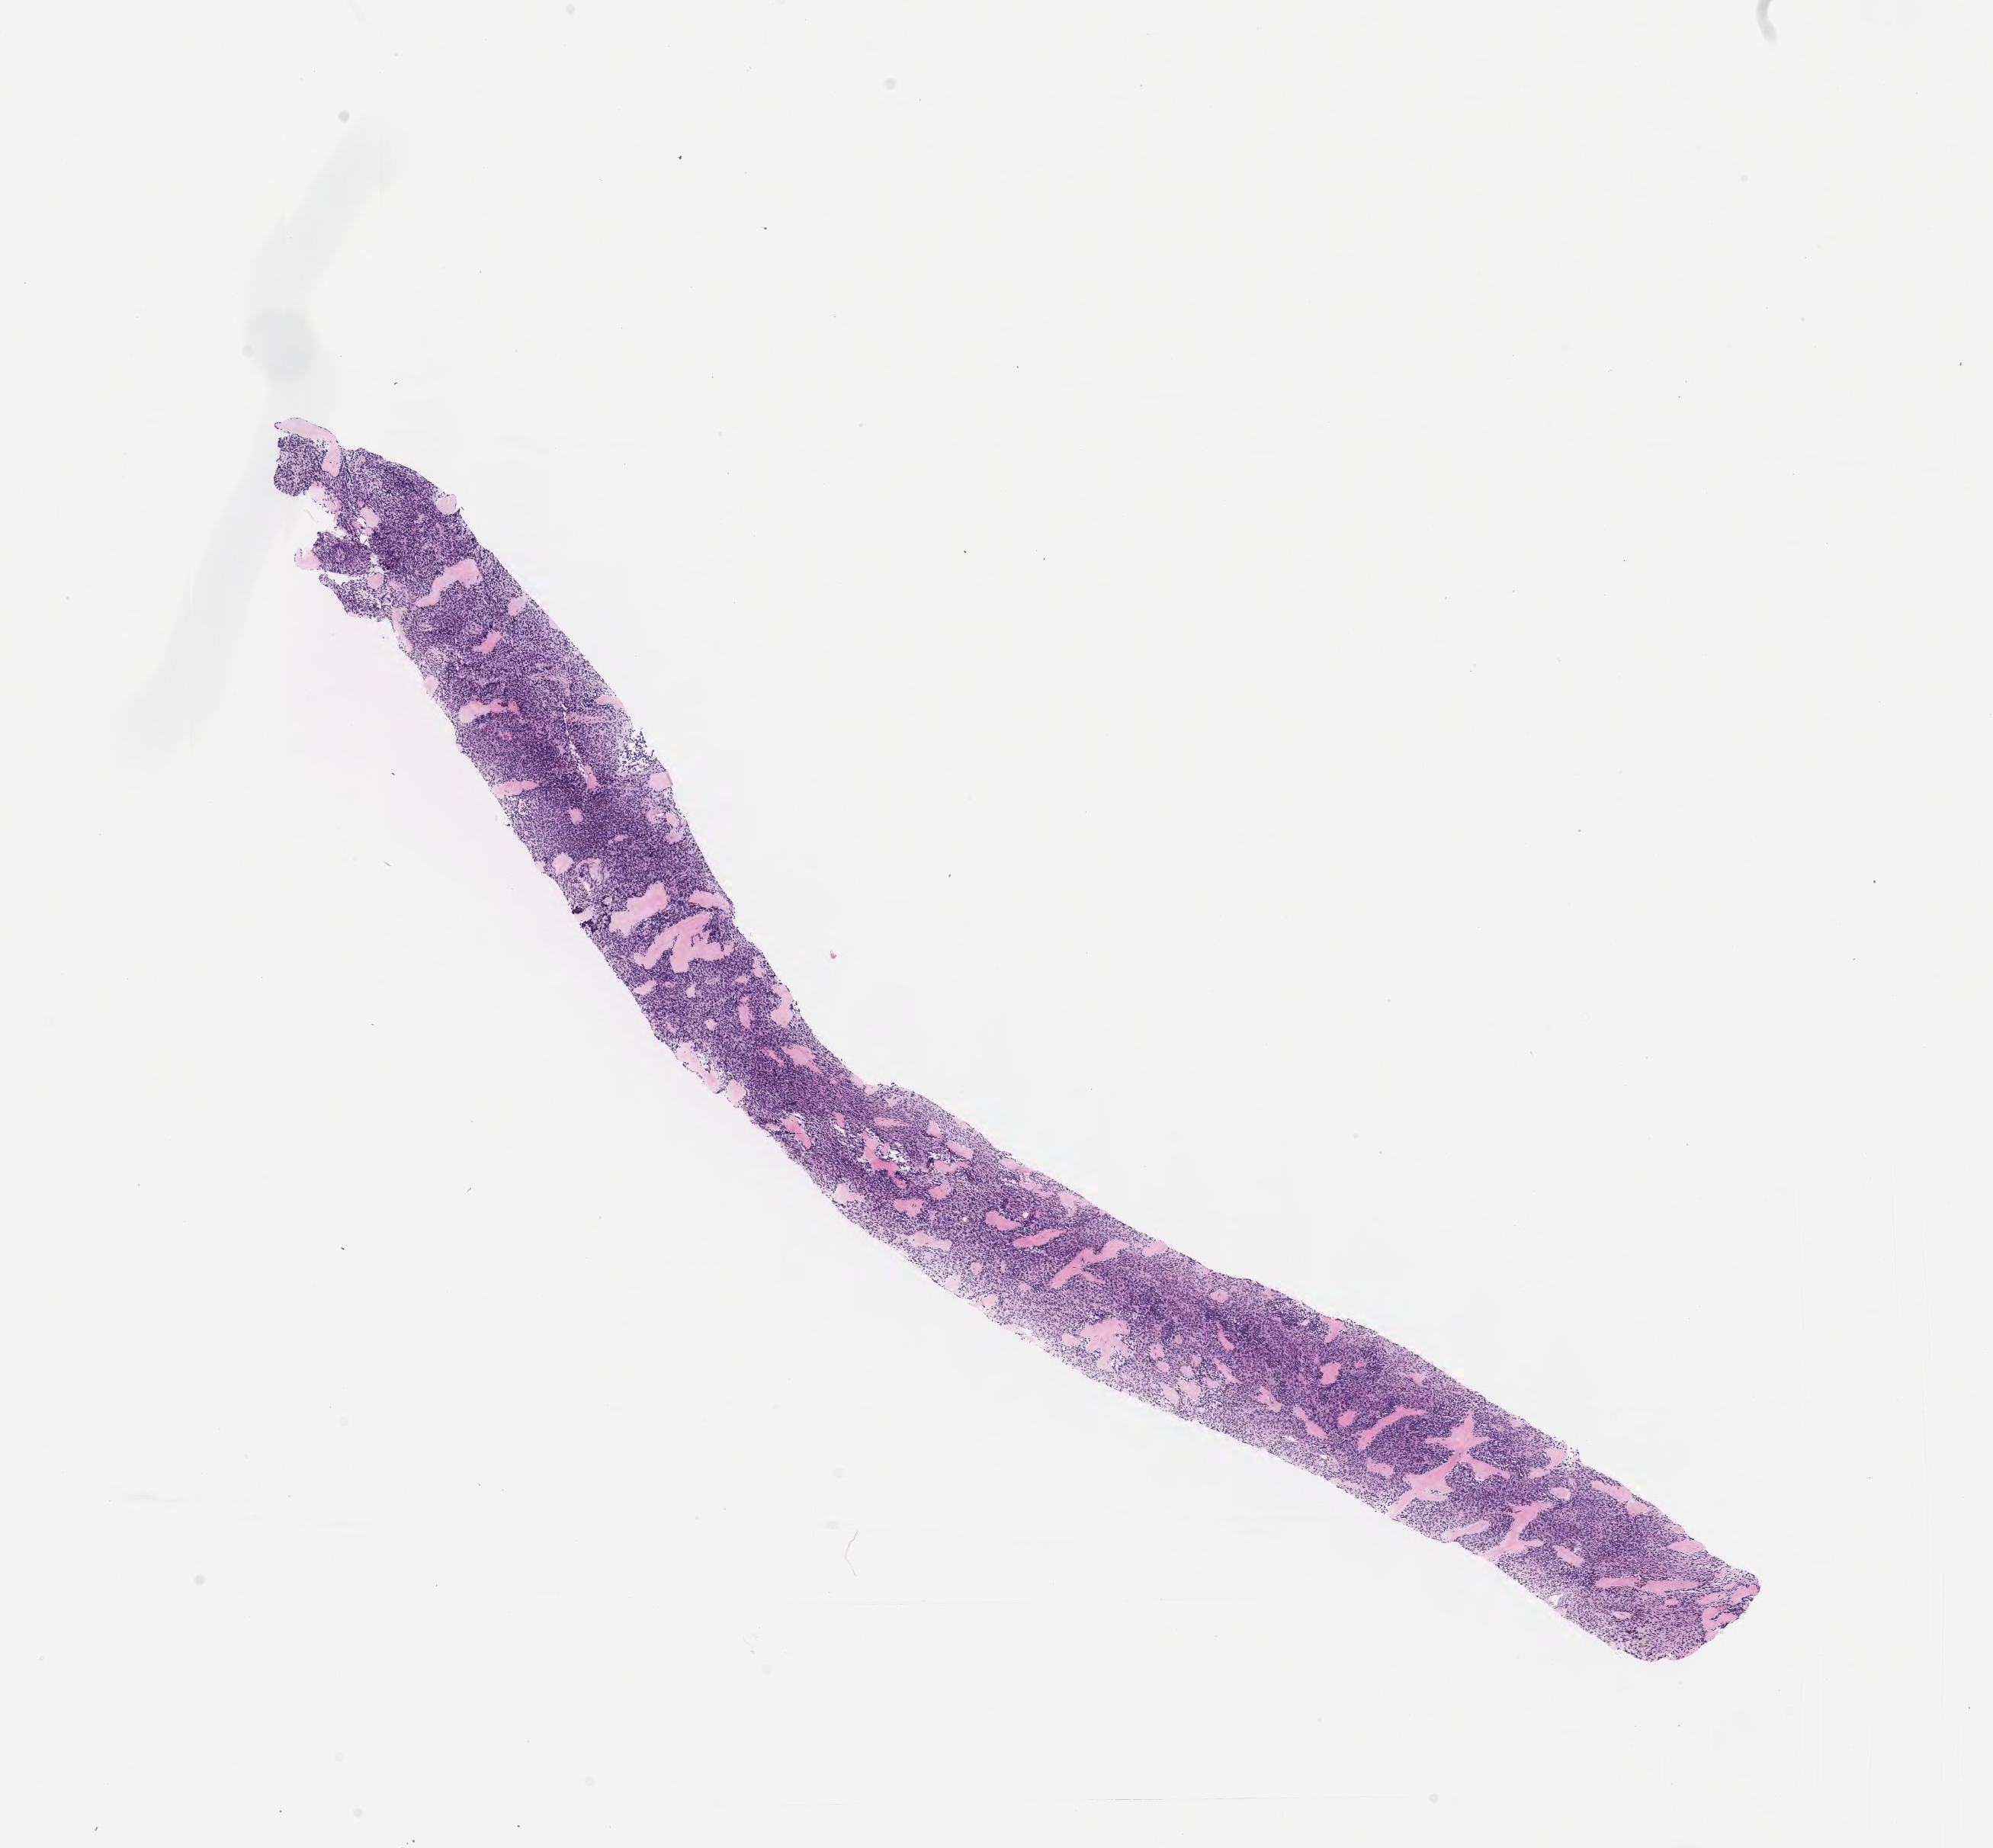
Whole-slide image, haematoxylin and eosin stain of tumor tissue from the soft tissue — shown as a low-resolution overview of the whole scanned area (about 10.6 x 9.8 mm); FFPE section. Patient female; age 84 months (7 years).
Recorded diagnosis: Undifferentiated sarcoma.